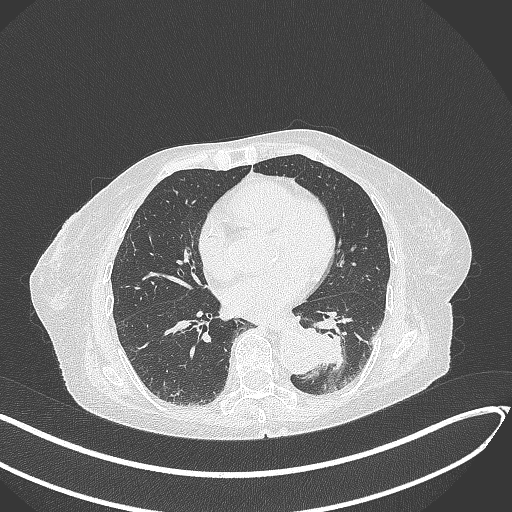
Chest CT, one axial slice; slice 103 of 324 in the series (ordered by position); 120 kVp; lung window (W 1500 / L -600 HU); 1 mm slice thickness; 512 × 512 image matrix. Female patient, age 82 years. Case-level facts recorded for this patient, not image findings: clinical TNM (as recorded): T1b N0 M1.
Annotated regions visible in this slice (rectangle marked by the reading radiologist):
- lung tumour (recorded histology: adenocarcinoma): bounding box <295,321,356,379> (left, top, right, bottom; pixels)